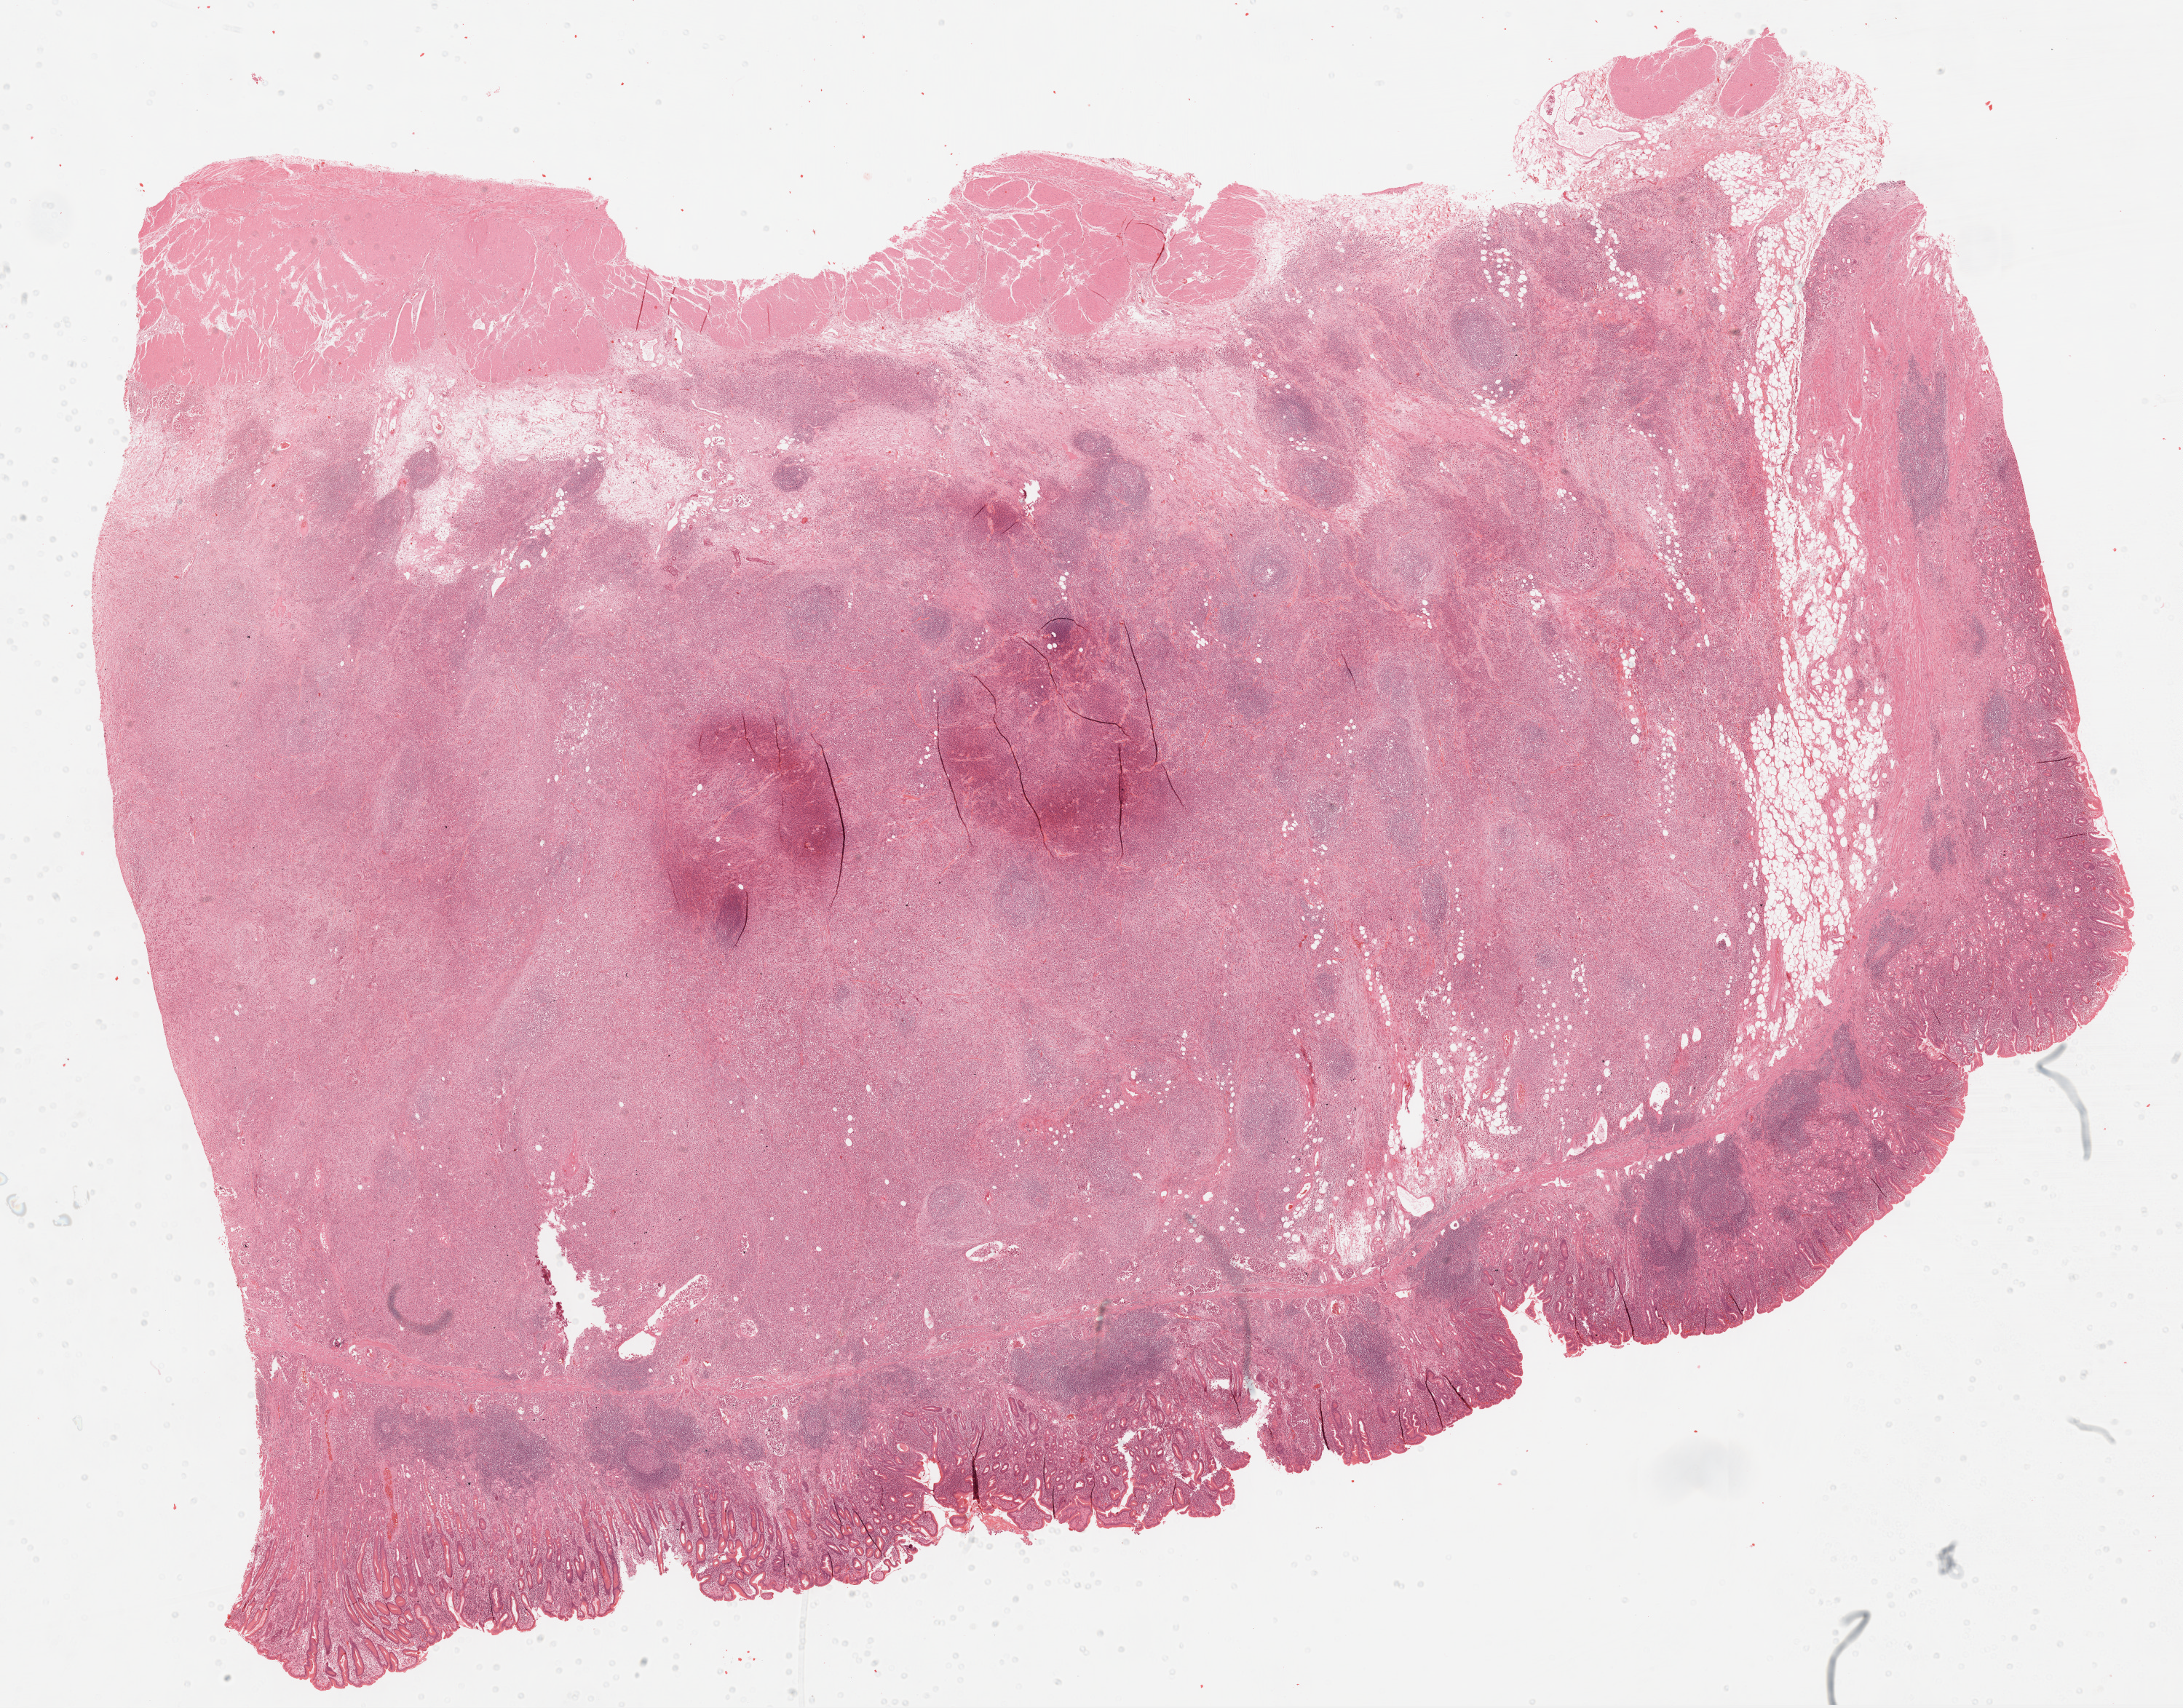
Whole-slide histology image, H&E — low-resolution overview of the scanned area, about 24.0 x 18.8 mm (slide scanned at 20x); formalin-fixed paraffin-embedded (FFPE) diagnostic section; stomach, primary tumour sample. Male, age 70 years at initial diagnosis. Histologic grade: G3 (poorly differentiated).
TNM: T3 N2 M0. AJCC pathologic stage: IIIB (6th edition). Pathologic diagnosis: Carcinoma, diffuse type (body of stomach).